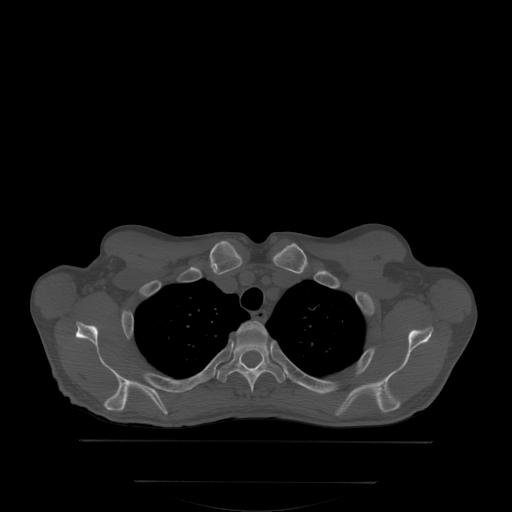
CT including the spine, one axial slice. Position 270 of 350 along the scan axis. Bone window (W 1800 / L 400 HU). 2.5 mm slice thickness. 512 × 512 image matrix, field of view 500 × 500 mm. Patient: male, 58 years. From the clinical record (not read from this slice): primary cancer: prostate; vertebrae with lytic lesions (as recorded): L1.
Outlined on this slice (semi-automatically segmented with operator editing):
- T2 vertebra: bounding box (x1, y1, x2, y2) in pixels: (246, 322, 266, 336)
- T3 vertebra: (216, 324, 286, 389)